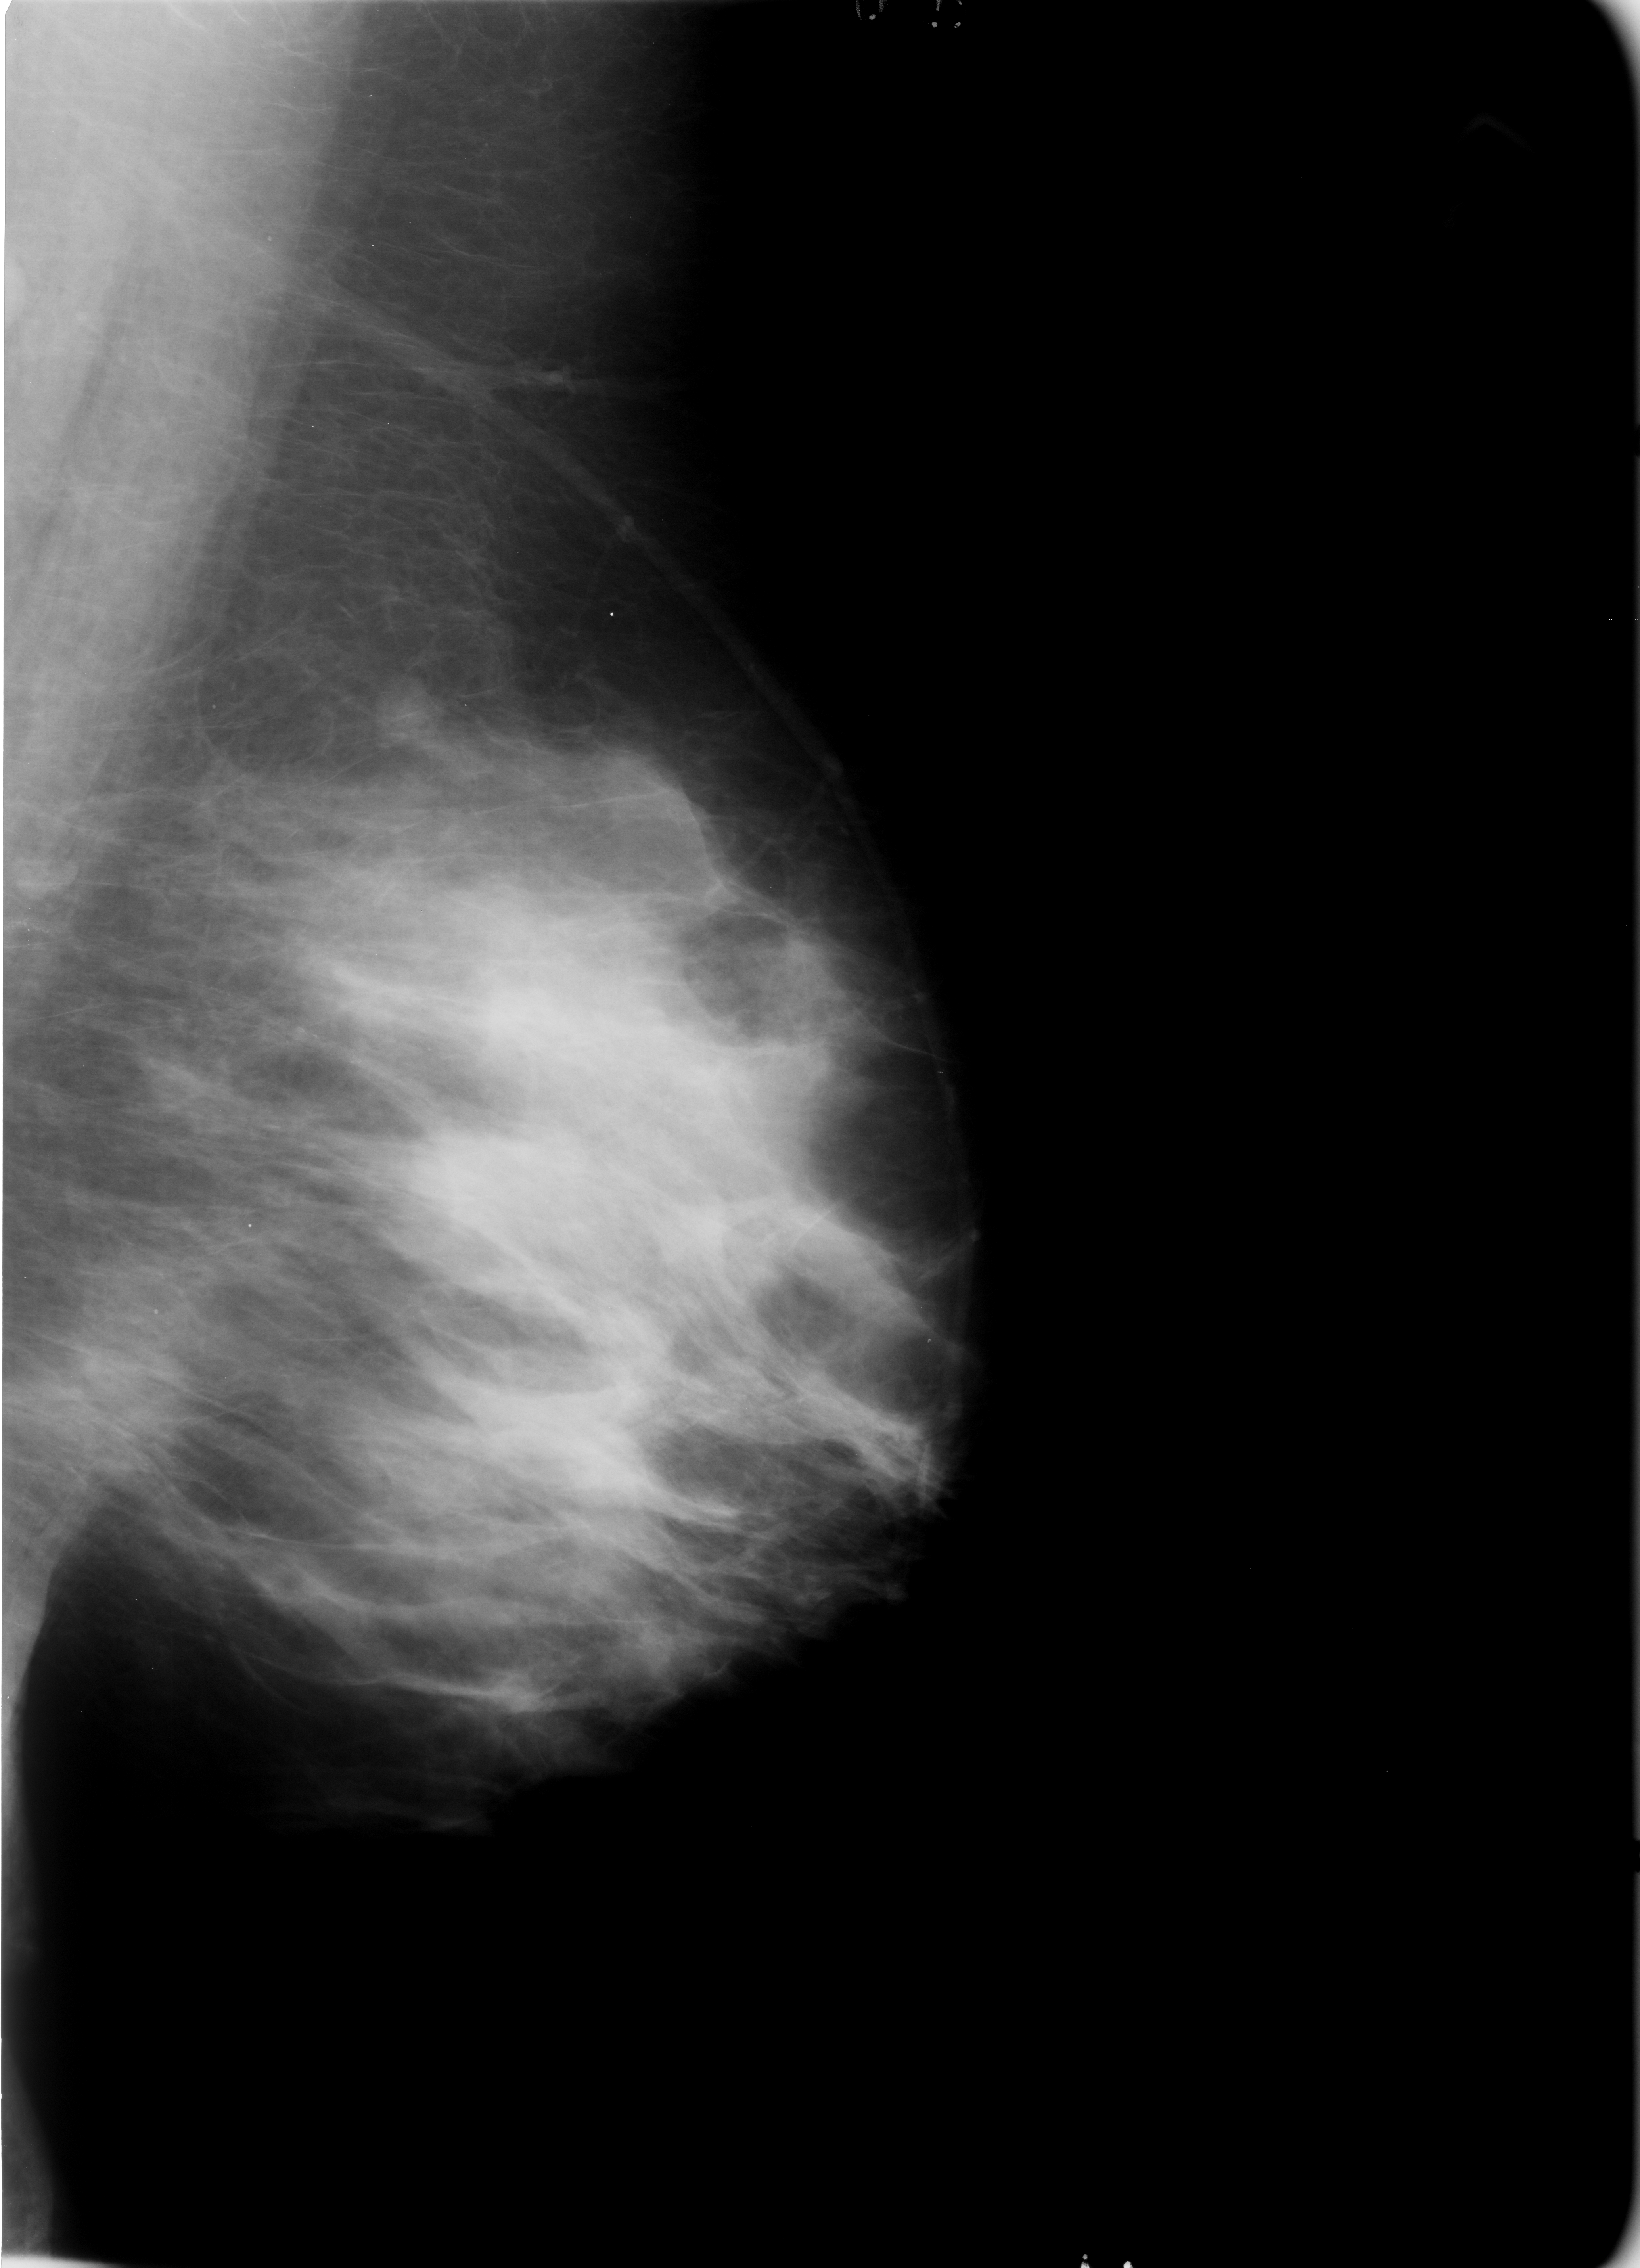
Scanned film-screen mammogram; left breast; MLO view; breast composition: heterogeneously dense (BI-RADS density category 3 of 4).
Finding: calcifications, morphology vascular; BI-RADS assessment category 2; subtlety rating 3 on a 1 (subtle) to 5 (obvious) scale; benign; no additional work-up was recommended (benign without callback).